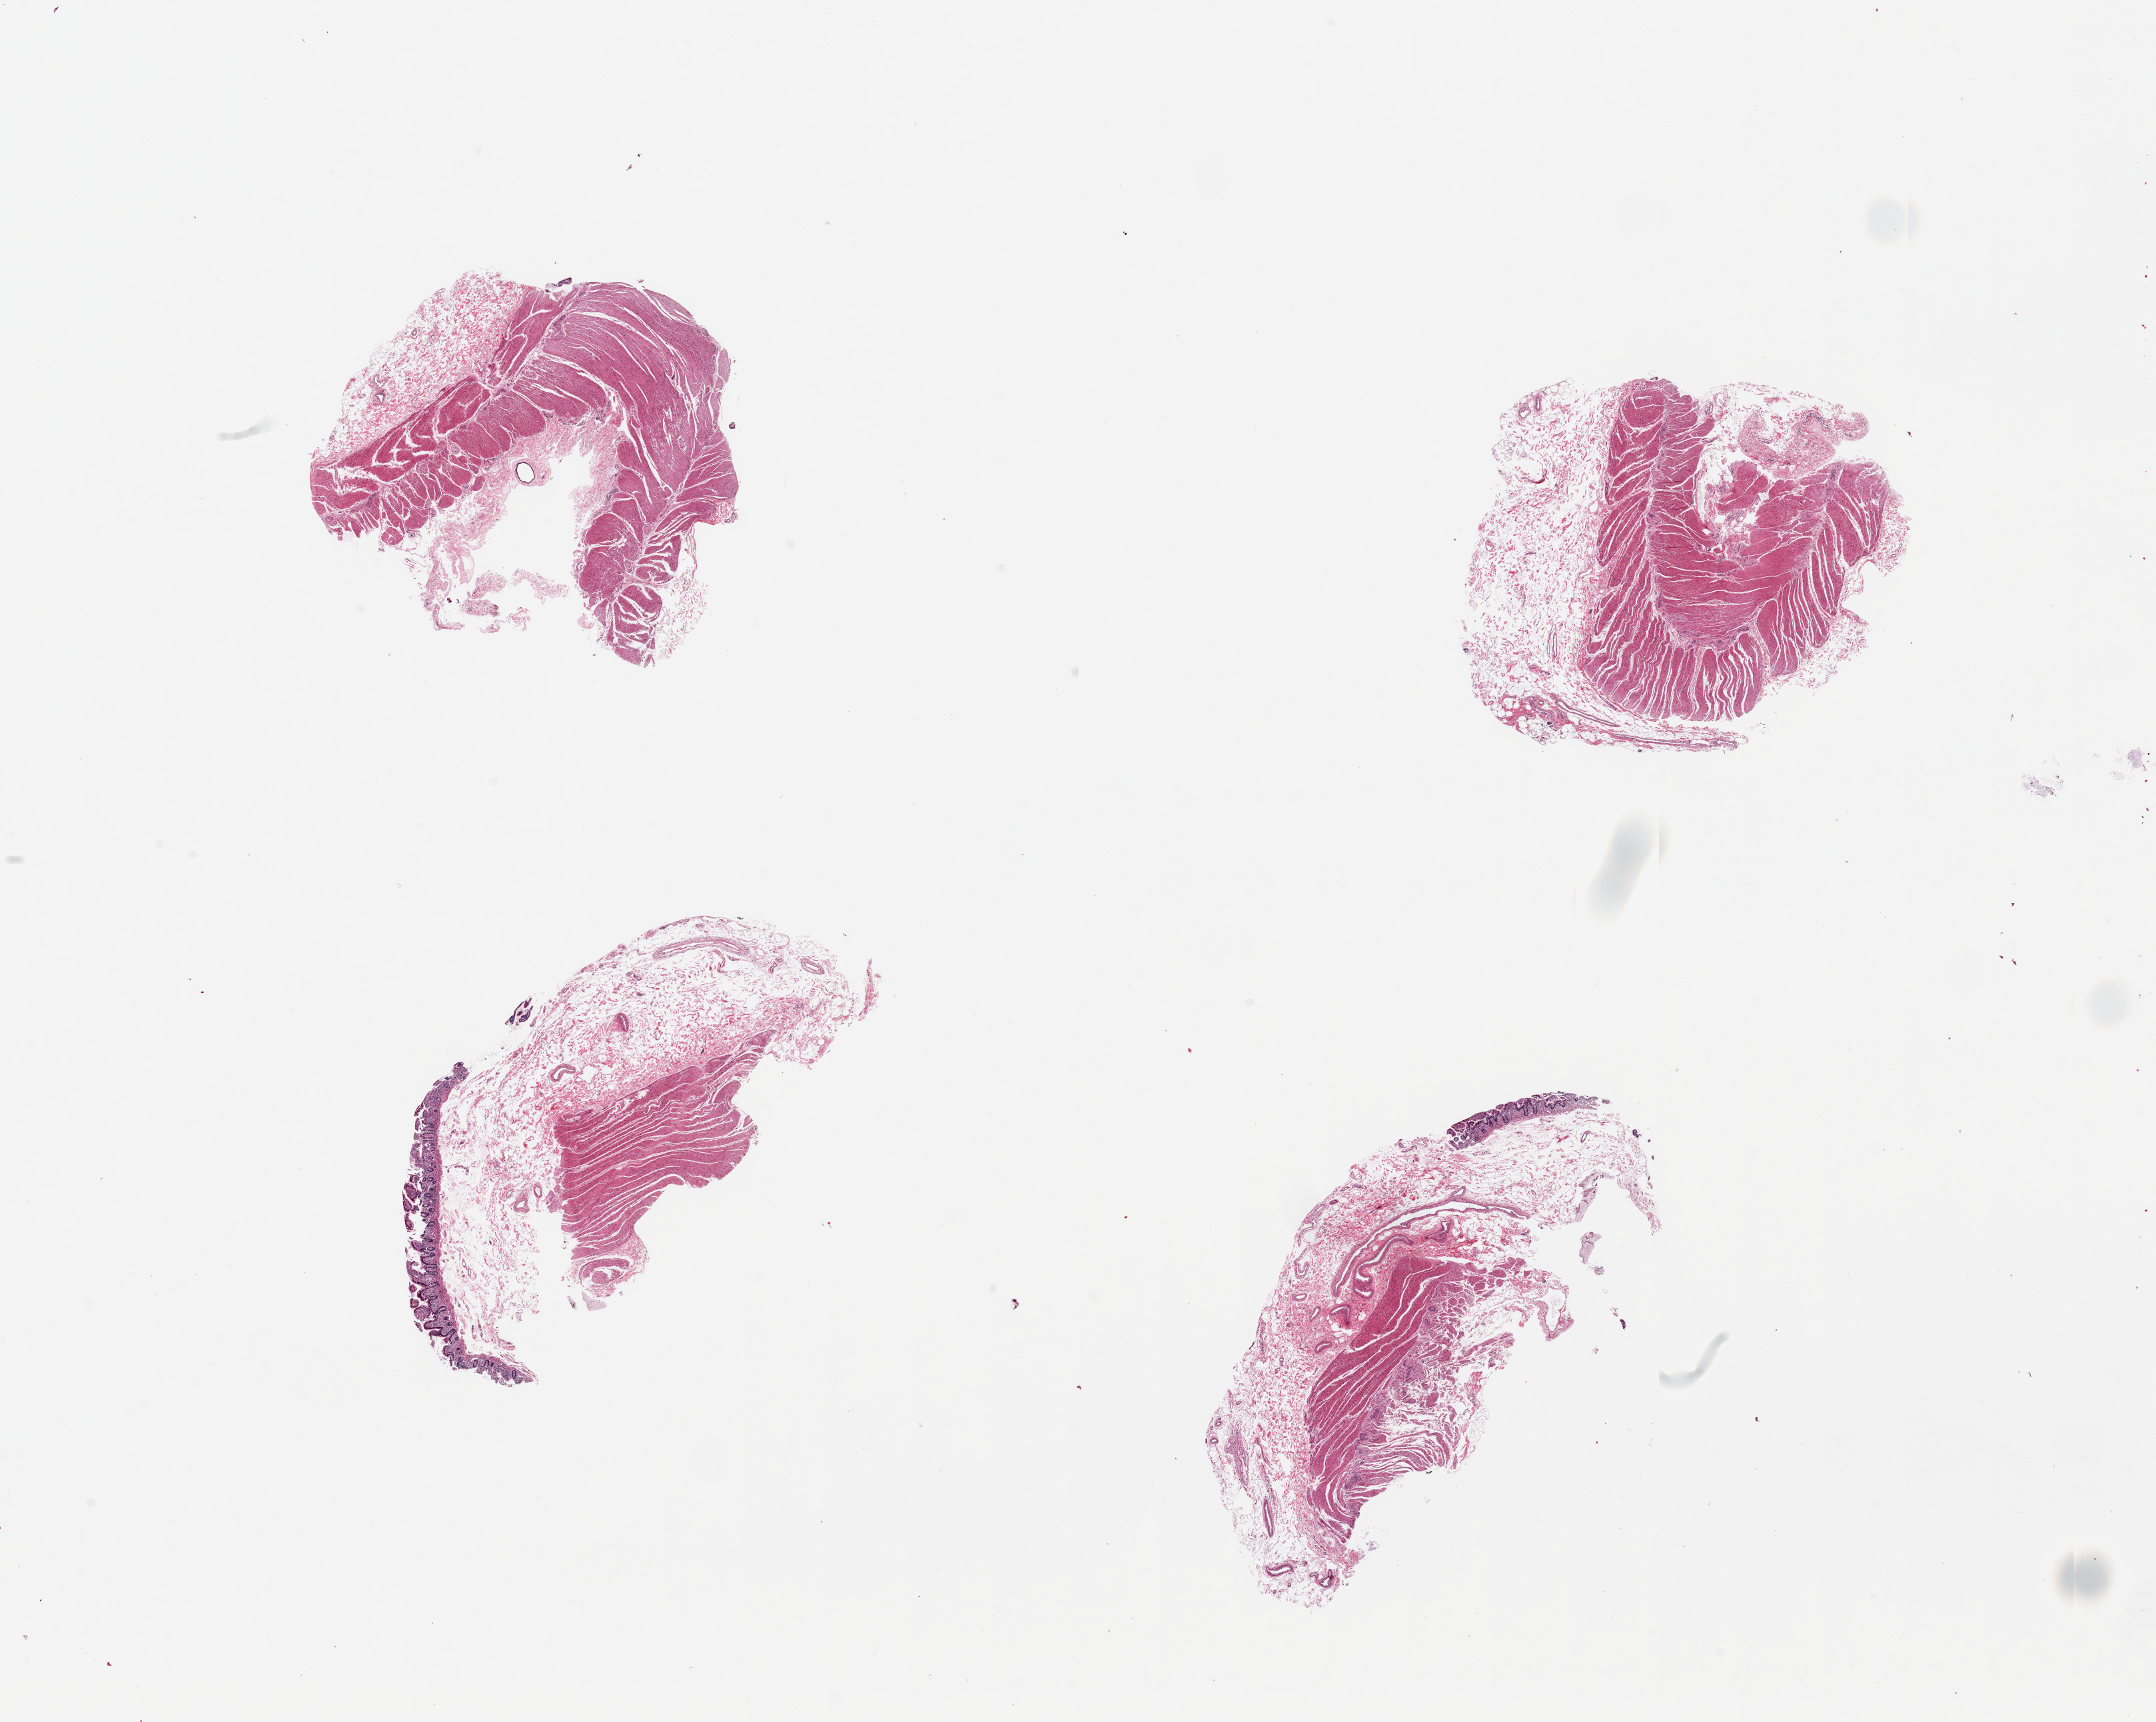
Digitized H&E-stained section, low-resolution overview of the scanned area, about 25.6 x 20.4 mm; PAXgene-fixed, paraffin-embedded tissue; section of ileum (target tissue); tissue donor sample. Donor: female.
• pathologist's review note for this sample: 4 pieces, ~10% mucosa, lymphoid elements, not follicles, not well preserved